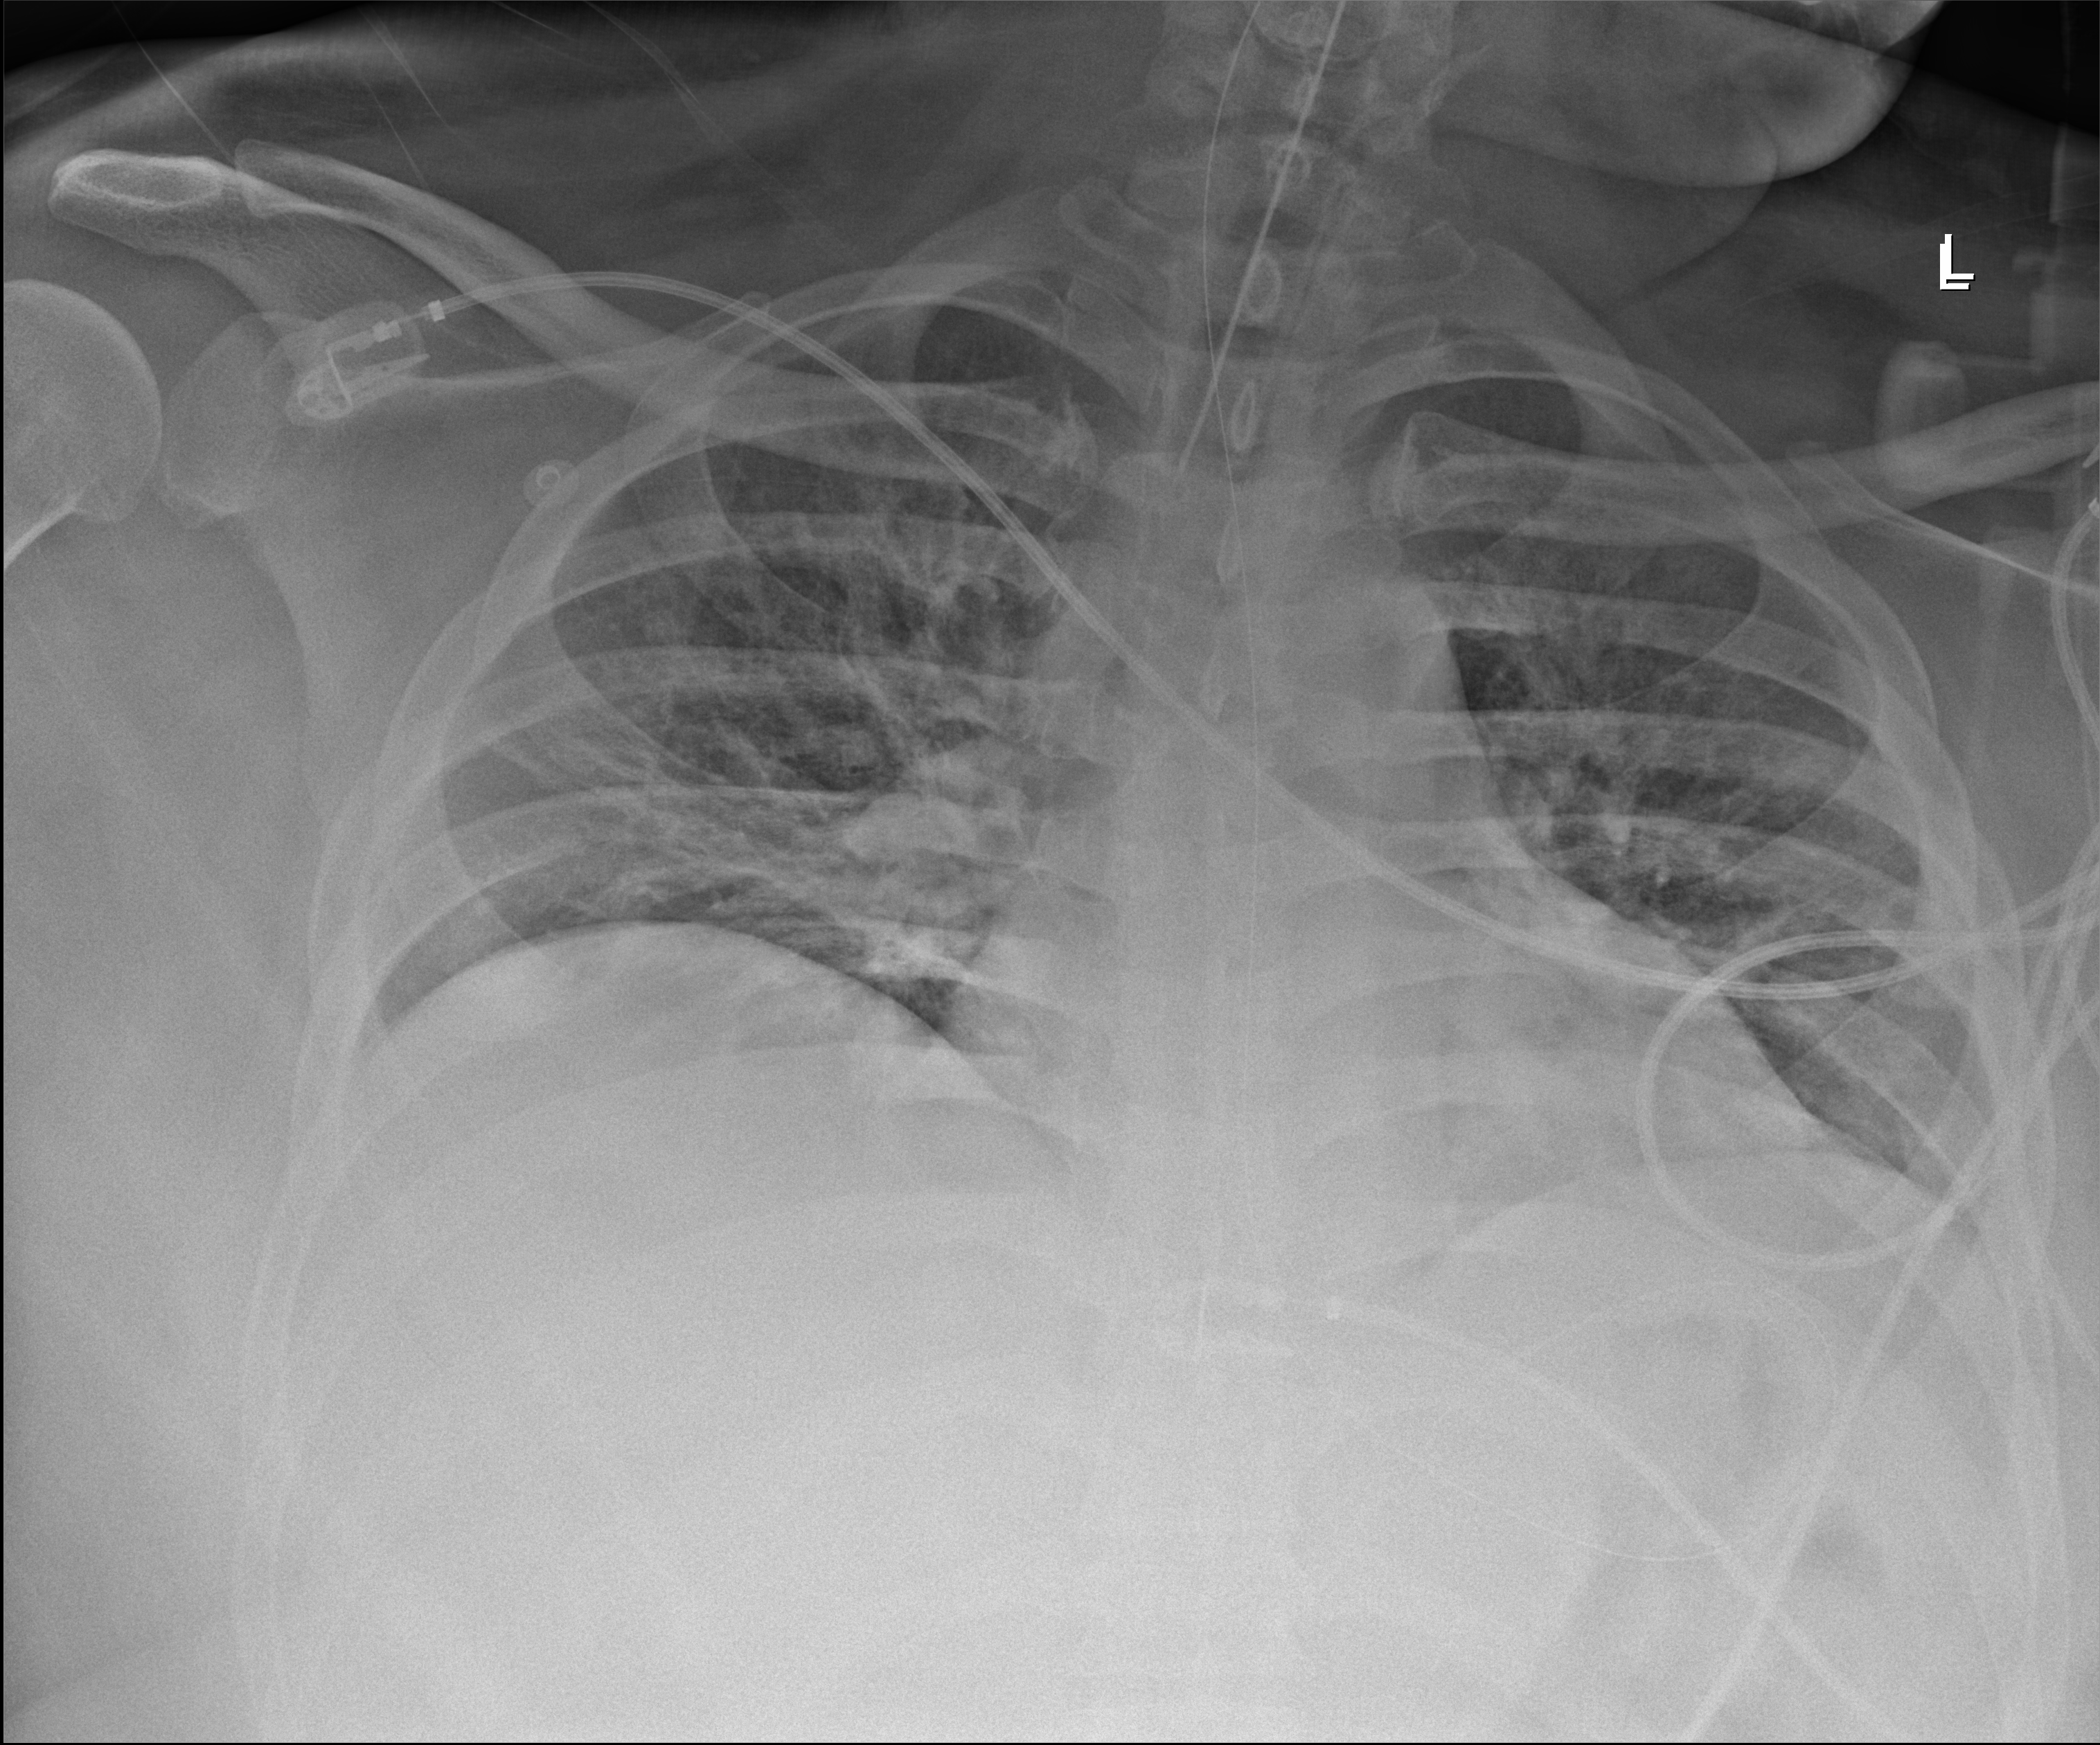
Bedside chest radiograph (digital radiography), anteroposterior (AP) projection. Male patient hospitalised with COVID-19, age 18–59 years.
Admission-level facts for this patient (not findings on this image; timing relative to this image not recorded): smoking status (admission record): never; admitted to intensive care during this hospital stay: yes; length of hospital stay: 69 days.